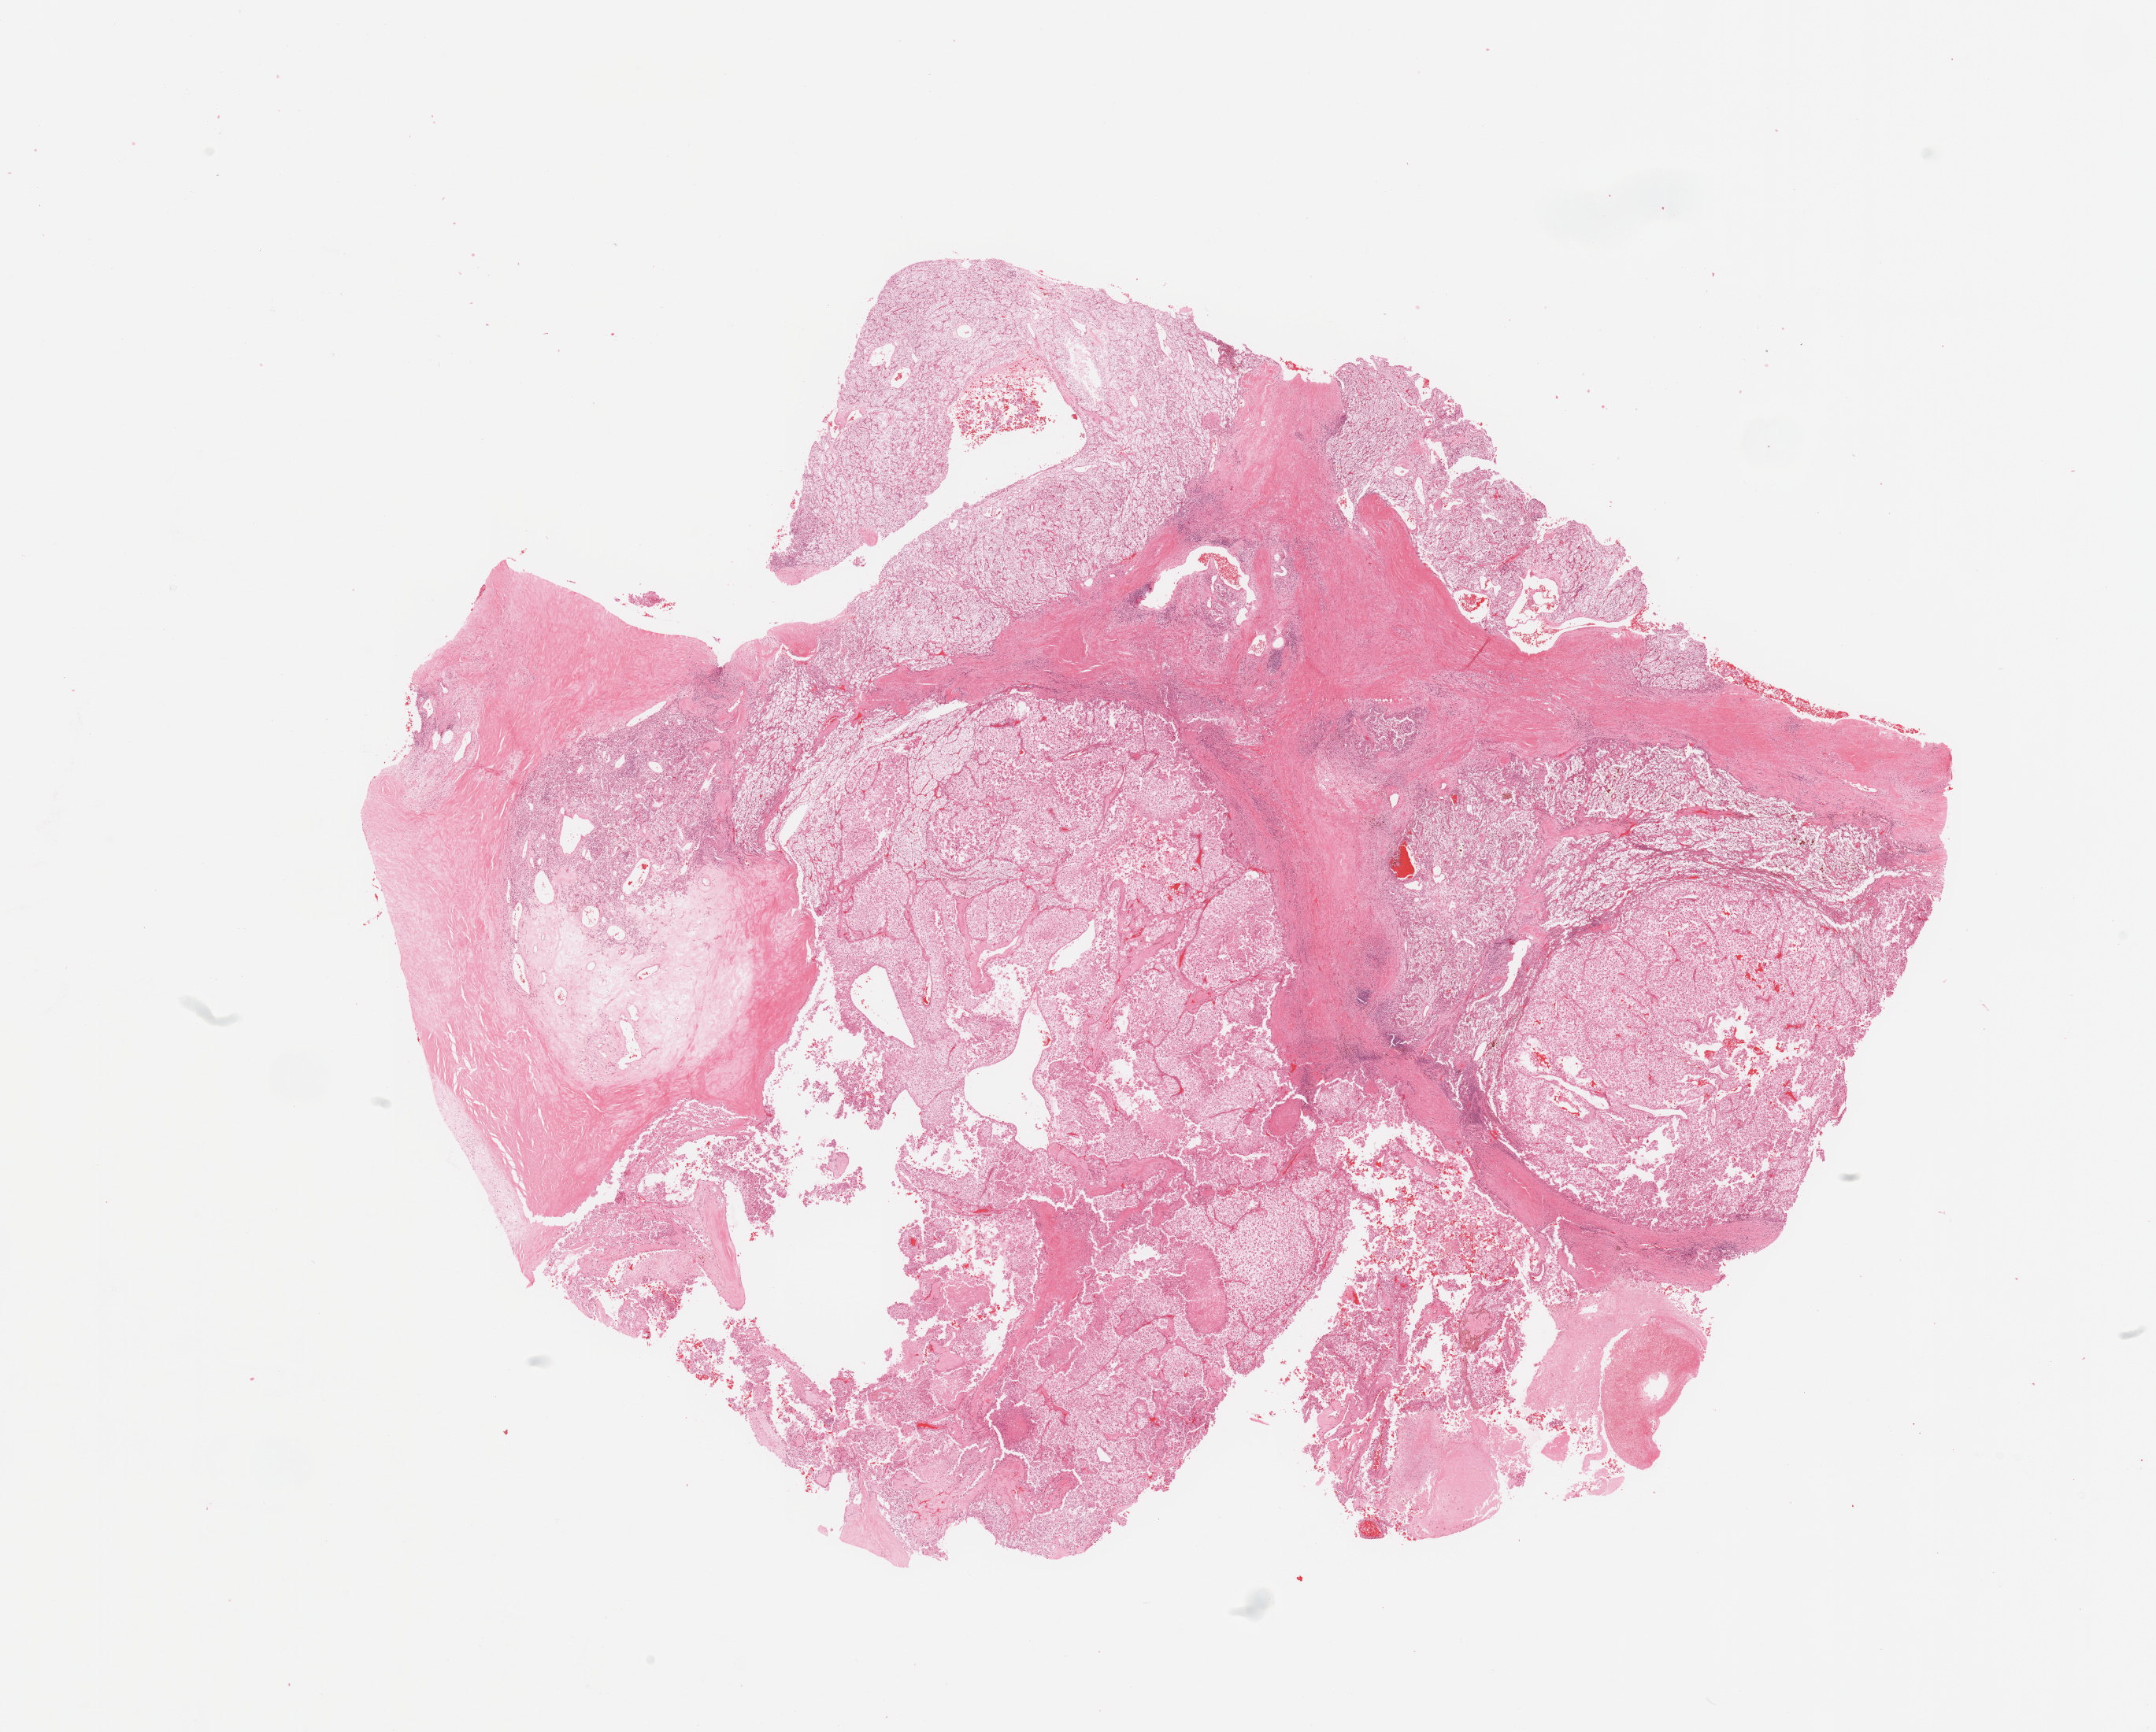
Digitized H&E-stained tissue section (whole slide) — shown as a low-resolution overview of the whole scanned area (about 21.7 x 17.4 mm, from a 20x scan). Kidney, tumour tissue. Male, 66 y/o. Histologic grade: G1 (well differentiated).
- histologic diagnosis: Renal cell carcinoma, NOS